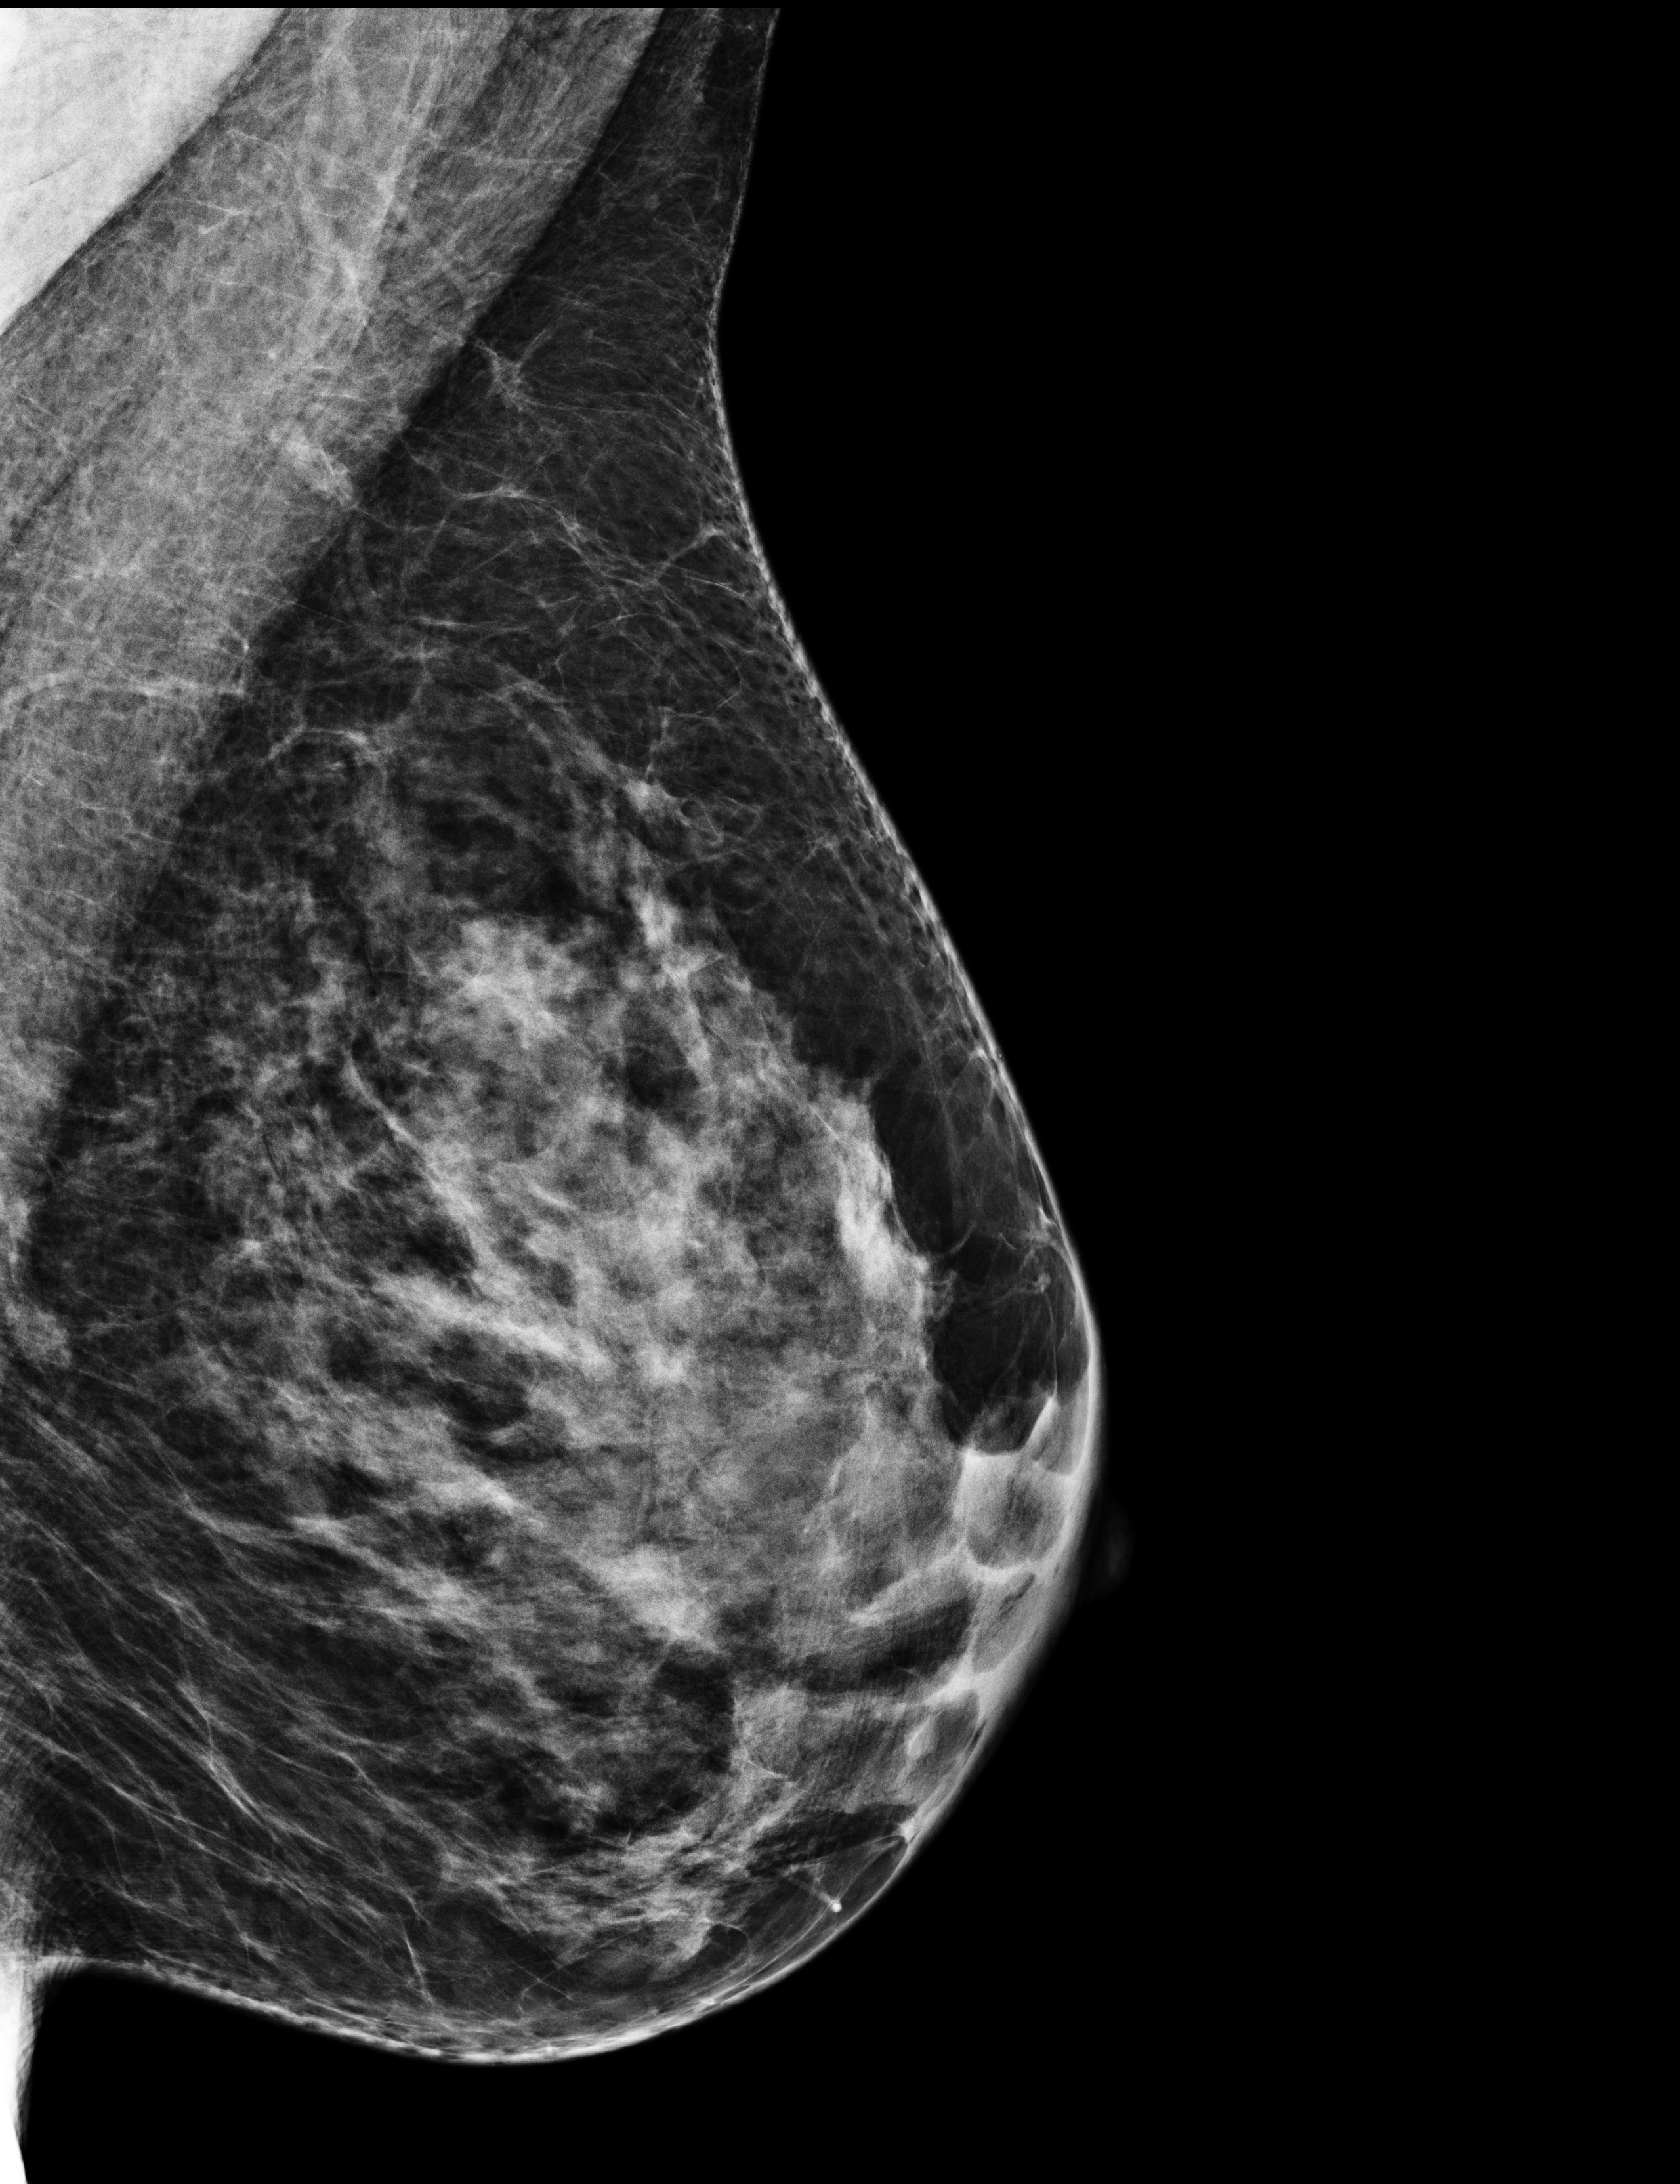
Full-field digital mammogram (FFDM); left breast; medio-lateral oblique projection; screening examination. Female patient, age 62 years.
Breast density at the screening exam (both breasts): heterogeneously dense (BI-RADS density category c). Final BI-RADS category for the screening round (tomosynthesis exam, both breasts): category 2. Recall: no recall after this screen.